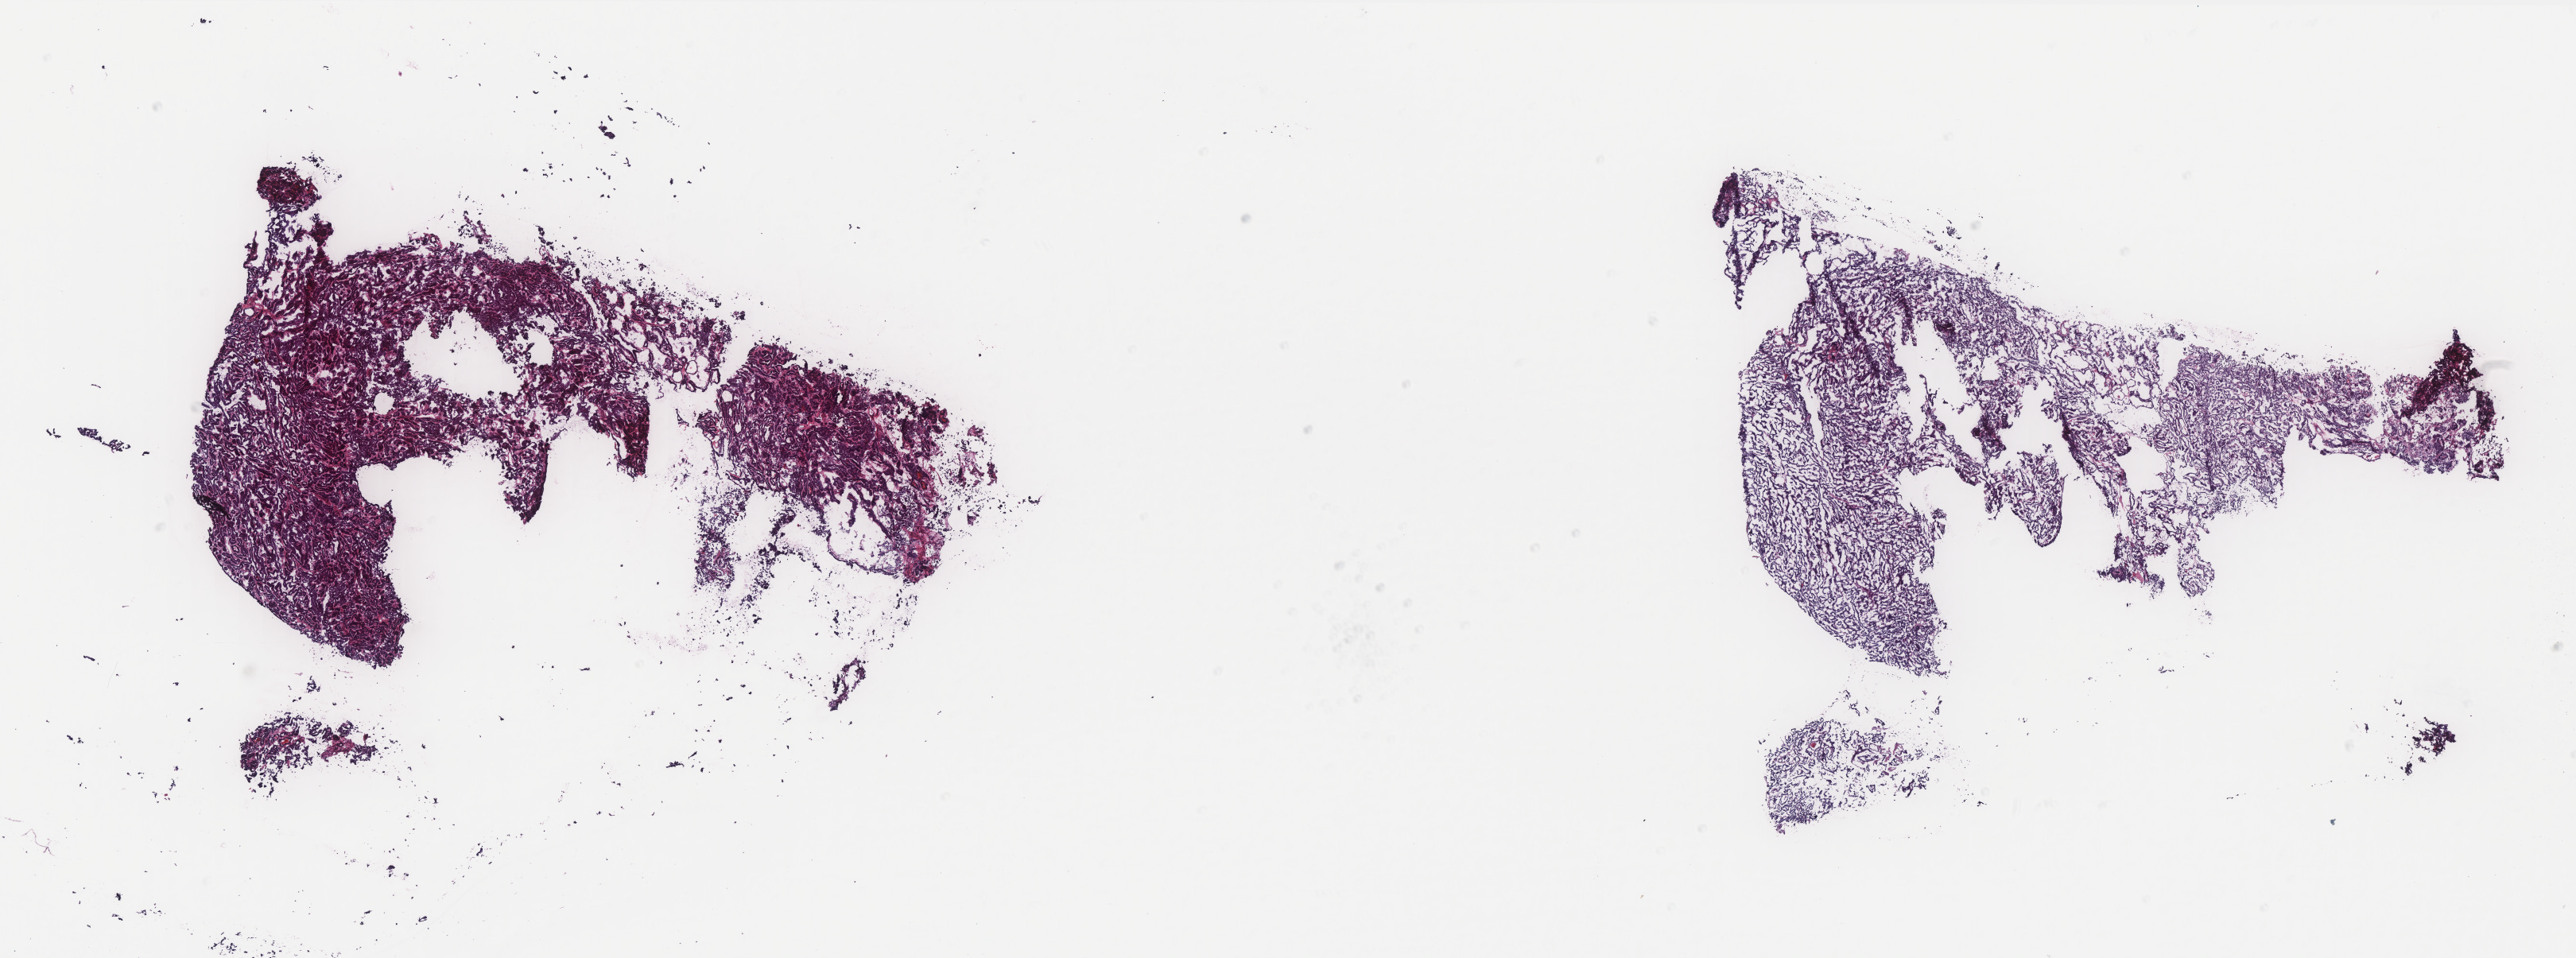
Whole-slide histology image, Hematoxylin and eosin (H&E) stained, a low-resolution overview of the entire scanned area, about 26.0 x 9.7 mm (from a 40x scan); frozen section from the top of the tissue portion; thyroid, primary tumour sample. Male patient; age at initial diagnosis 58 years. Composition of this section per pathologist review: tumour cells 85%, tumour nuclei 85%.
Diagnosis: Papillary adenocarcinoma, NOS (thyroid gland).